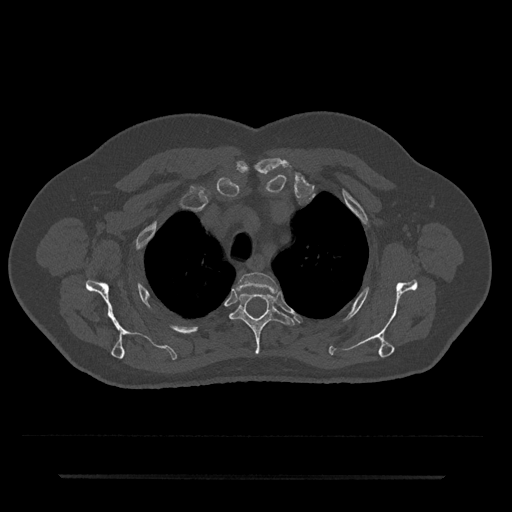
CT including the spine, one axial slice; slice 573 of 797 in the series (ordered by position); reconstruction kernel Br40s/3; 120 kVp; bone window (W 1800 / L 400 HU); 0.5 mm slice thickness; 512 × 512 image matrix. Male patient, age 69 years. From the clinical record (not read from this slice): primary cancer: prostate.
Annotated regions visible in this slice (semi-automatic segmentation, software-assisted and operator-edited):
- T2 vertebra: bounding box <237,272,278,294> (left, top, right, bottom; pixels)
- T3 vertebra: <230,293,295,354>